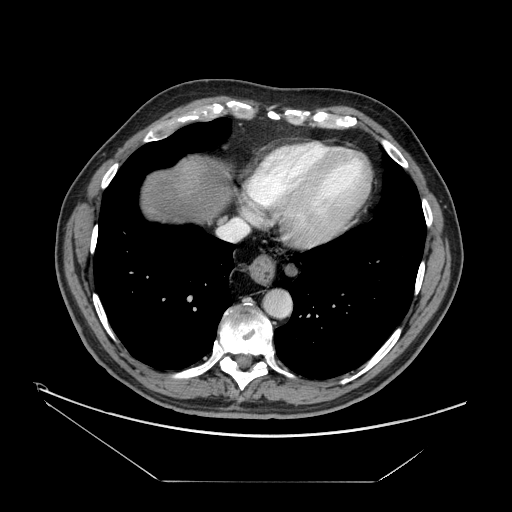
Contrast-enhanced abdominal CT, one axial slice. Slice 151 of 161 in the series (ordered by position). Reconstruction kernel STANDARD. Intravenous contrast given. Soft-tissue window (W 400 / L 40 HU). 2.5 mm slice thickness. 512 × 512 image matrix, field of view 440 × 440 mm. Male patient, age 65 years. Case-level facts recorded for this patient, not image findings: diagnosis: colorectal cancer liver metastases, imaged before liver resection; multiple liver metastases: yes; largest metastasis: 4.2 cm; disease in both lobes: yes.
Outlined on this slice (expert manual segmentation):
- hepatic veins: bounding box [x1, y1, x2, y2] px = [218, 162, 267, 241]
- liver: [141, 156, 229, 222]
- planned liver remnant (the part of the liver to remain after resection): [141, 155, 229, 223]